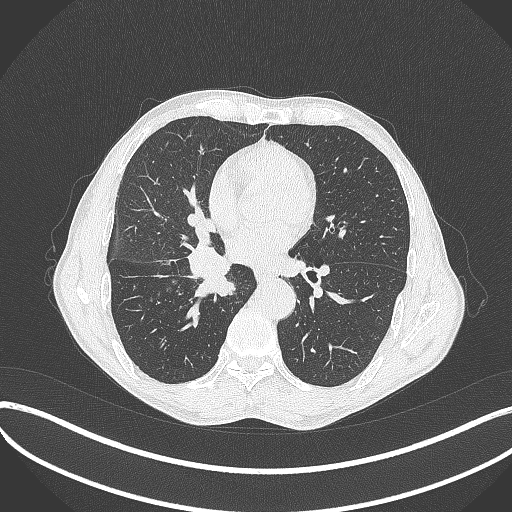
Chest CT, one axial slice; position 204 of 481 along the scan axis; reconstruction kernel B70f; 120 kVp; lung window (W 1500 / L -600 HU); 1 mm slice thickness; 512 × 512 image matrix, field of view 400 × 400 mm. Patient: male, 65 years. From the clinical record (not read from this slice): clinical TNM (as recorded): T2a N0 M0.
Annotated regions visible in this slice (bounding box drawn by a radiologist):
- lung tumour (recorded histology: squamous cell carcinoma): bounding box [x1, y1, x2, y2] px = [183, 236, 244, 300]